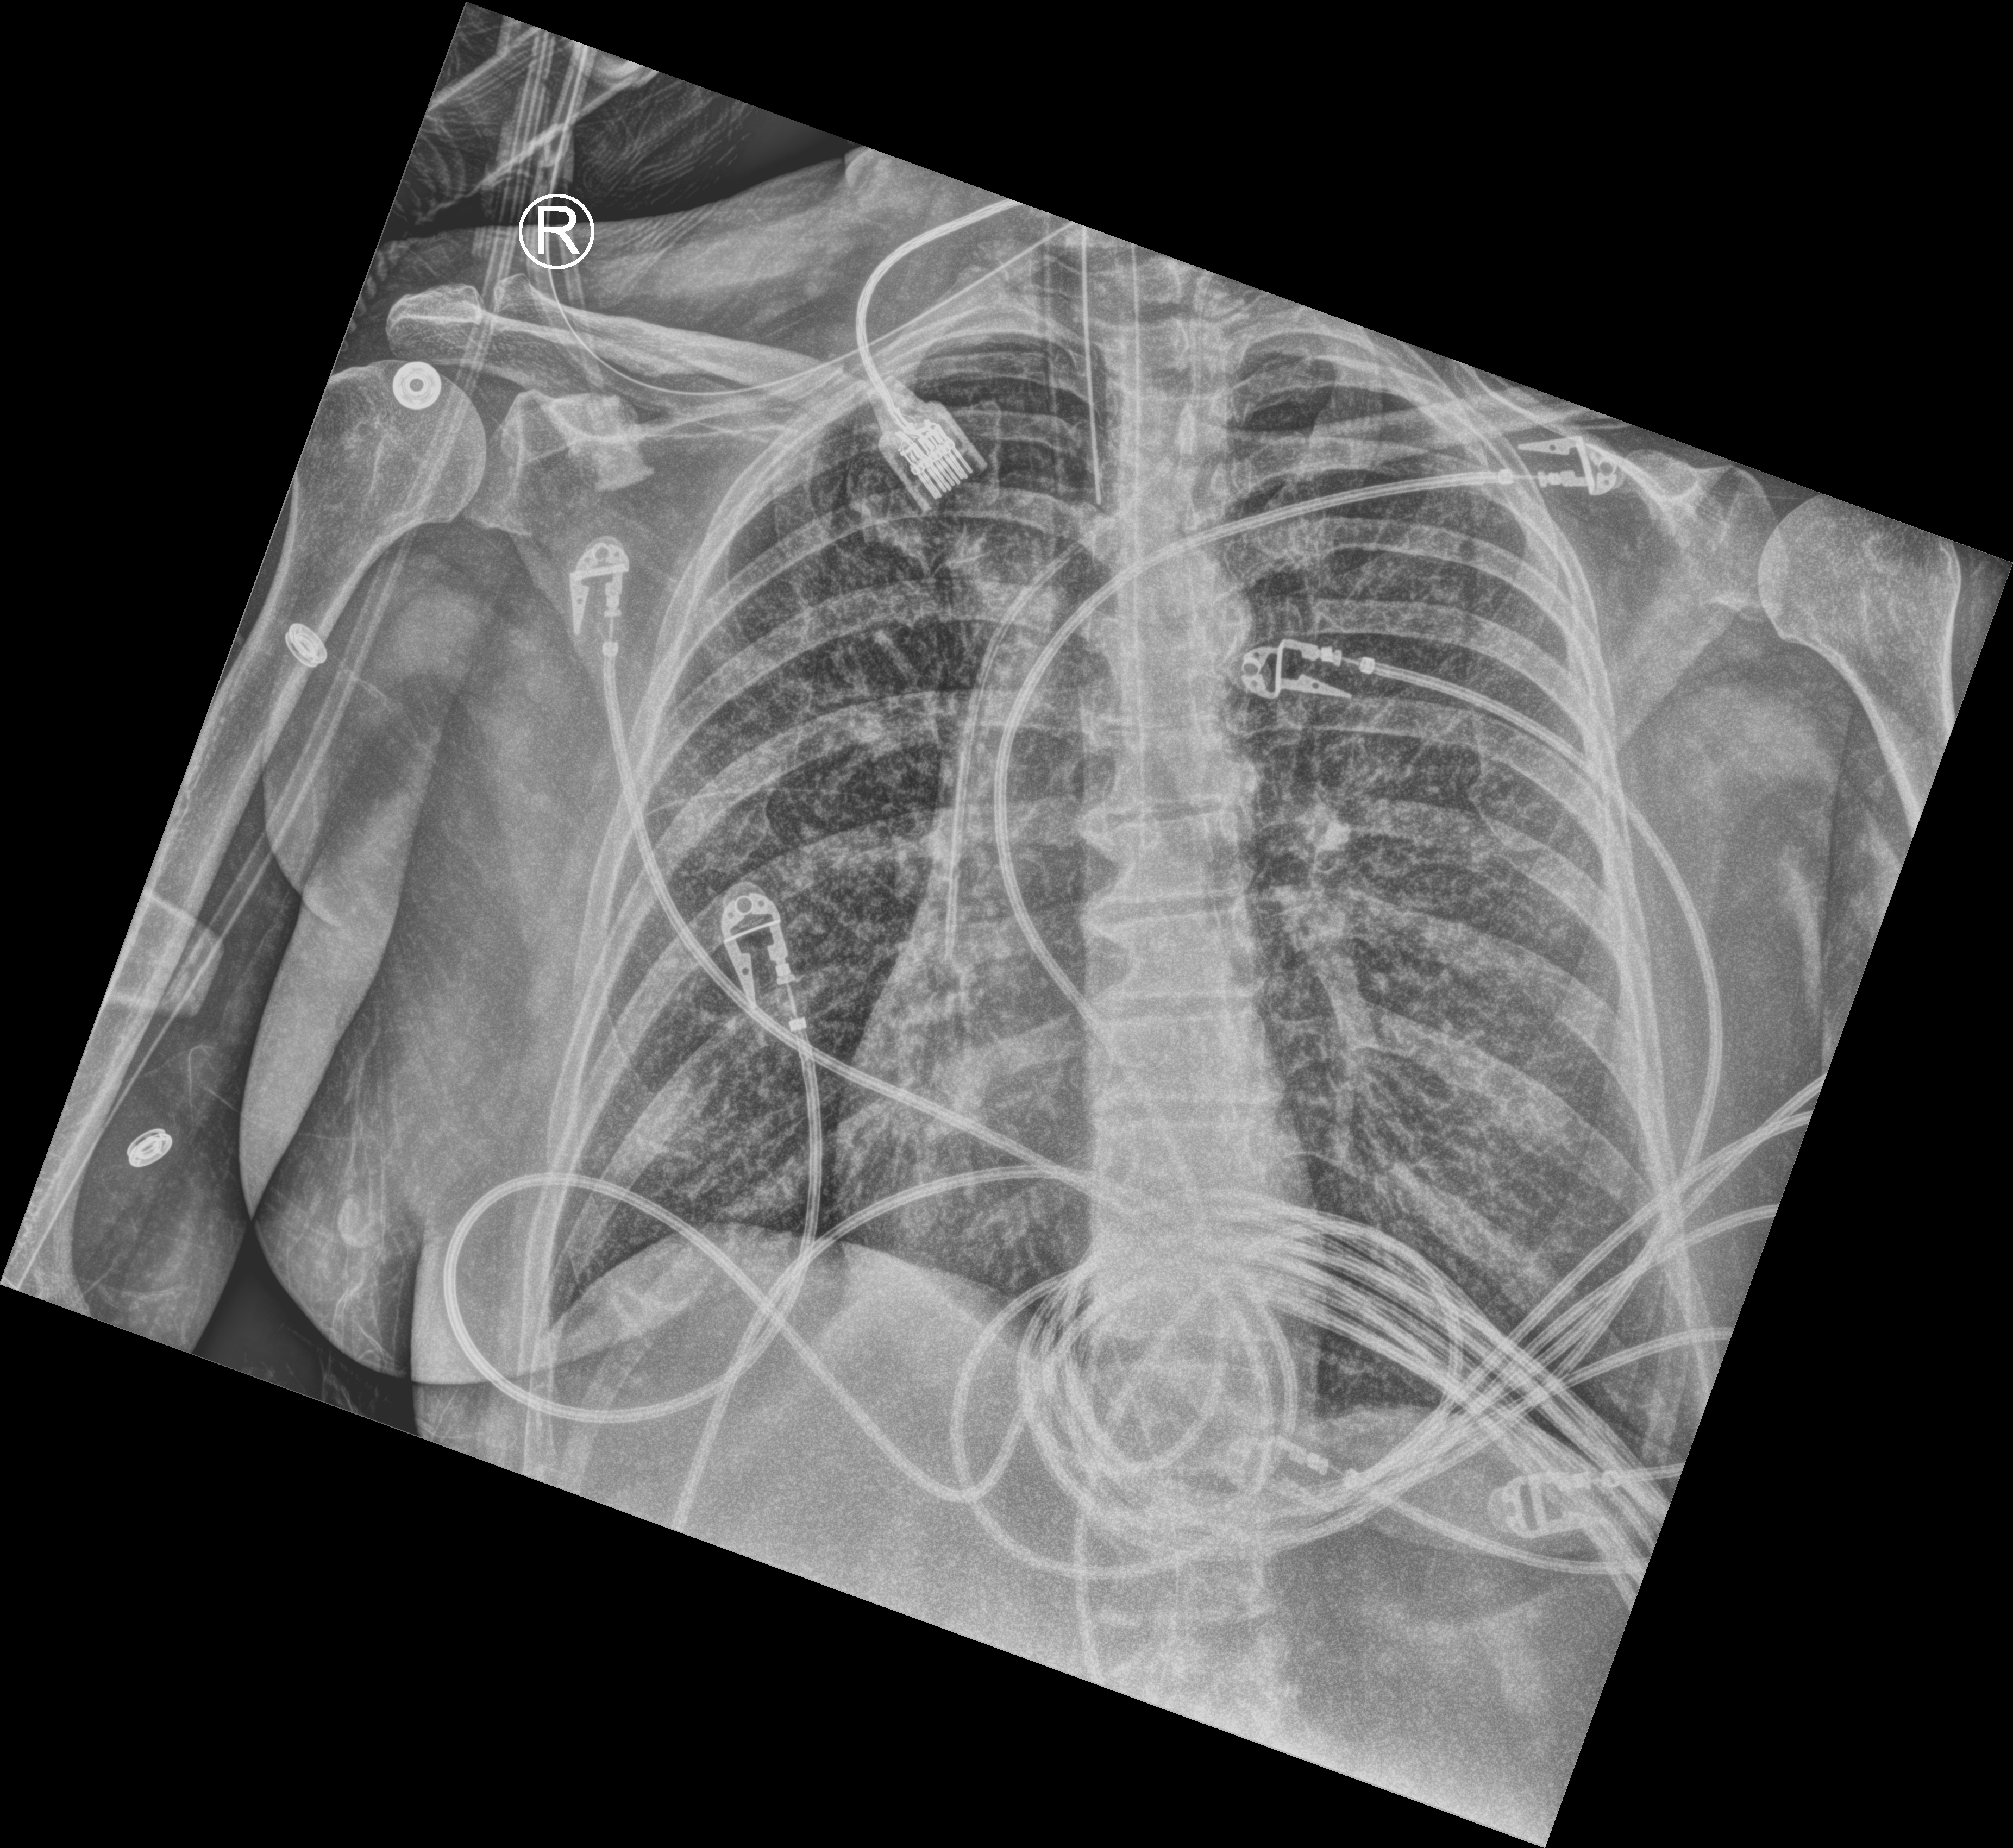
Bedside chest radiograph (computed radiography); anteroposterior (AP) projection. Female patient hospitalised with COVID-19, age 60–74 years.
Hospital-stay facts (about this admission, not read from this image; timing relative to this image not recorded): mechanically ventilated during this hospital stay: yes; chronic kidney disease (admission record): no.